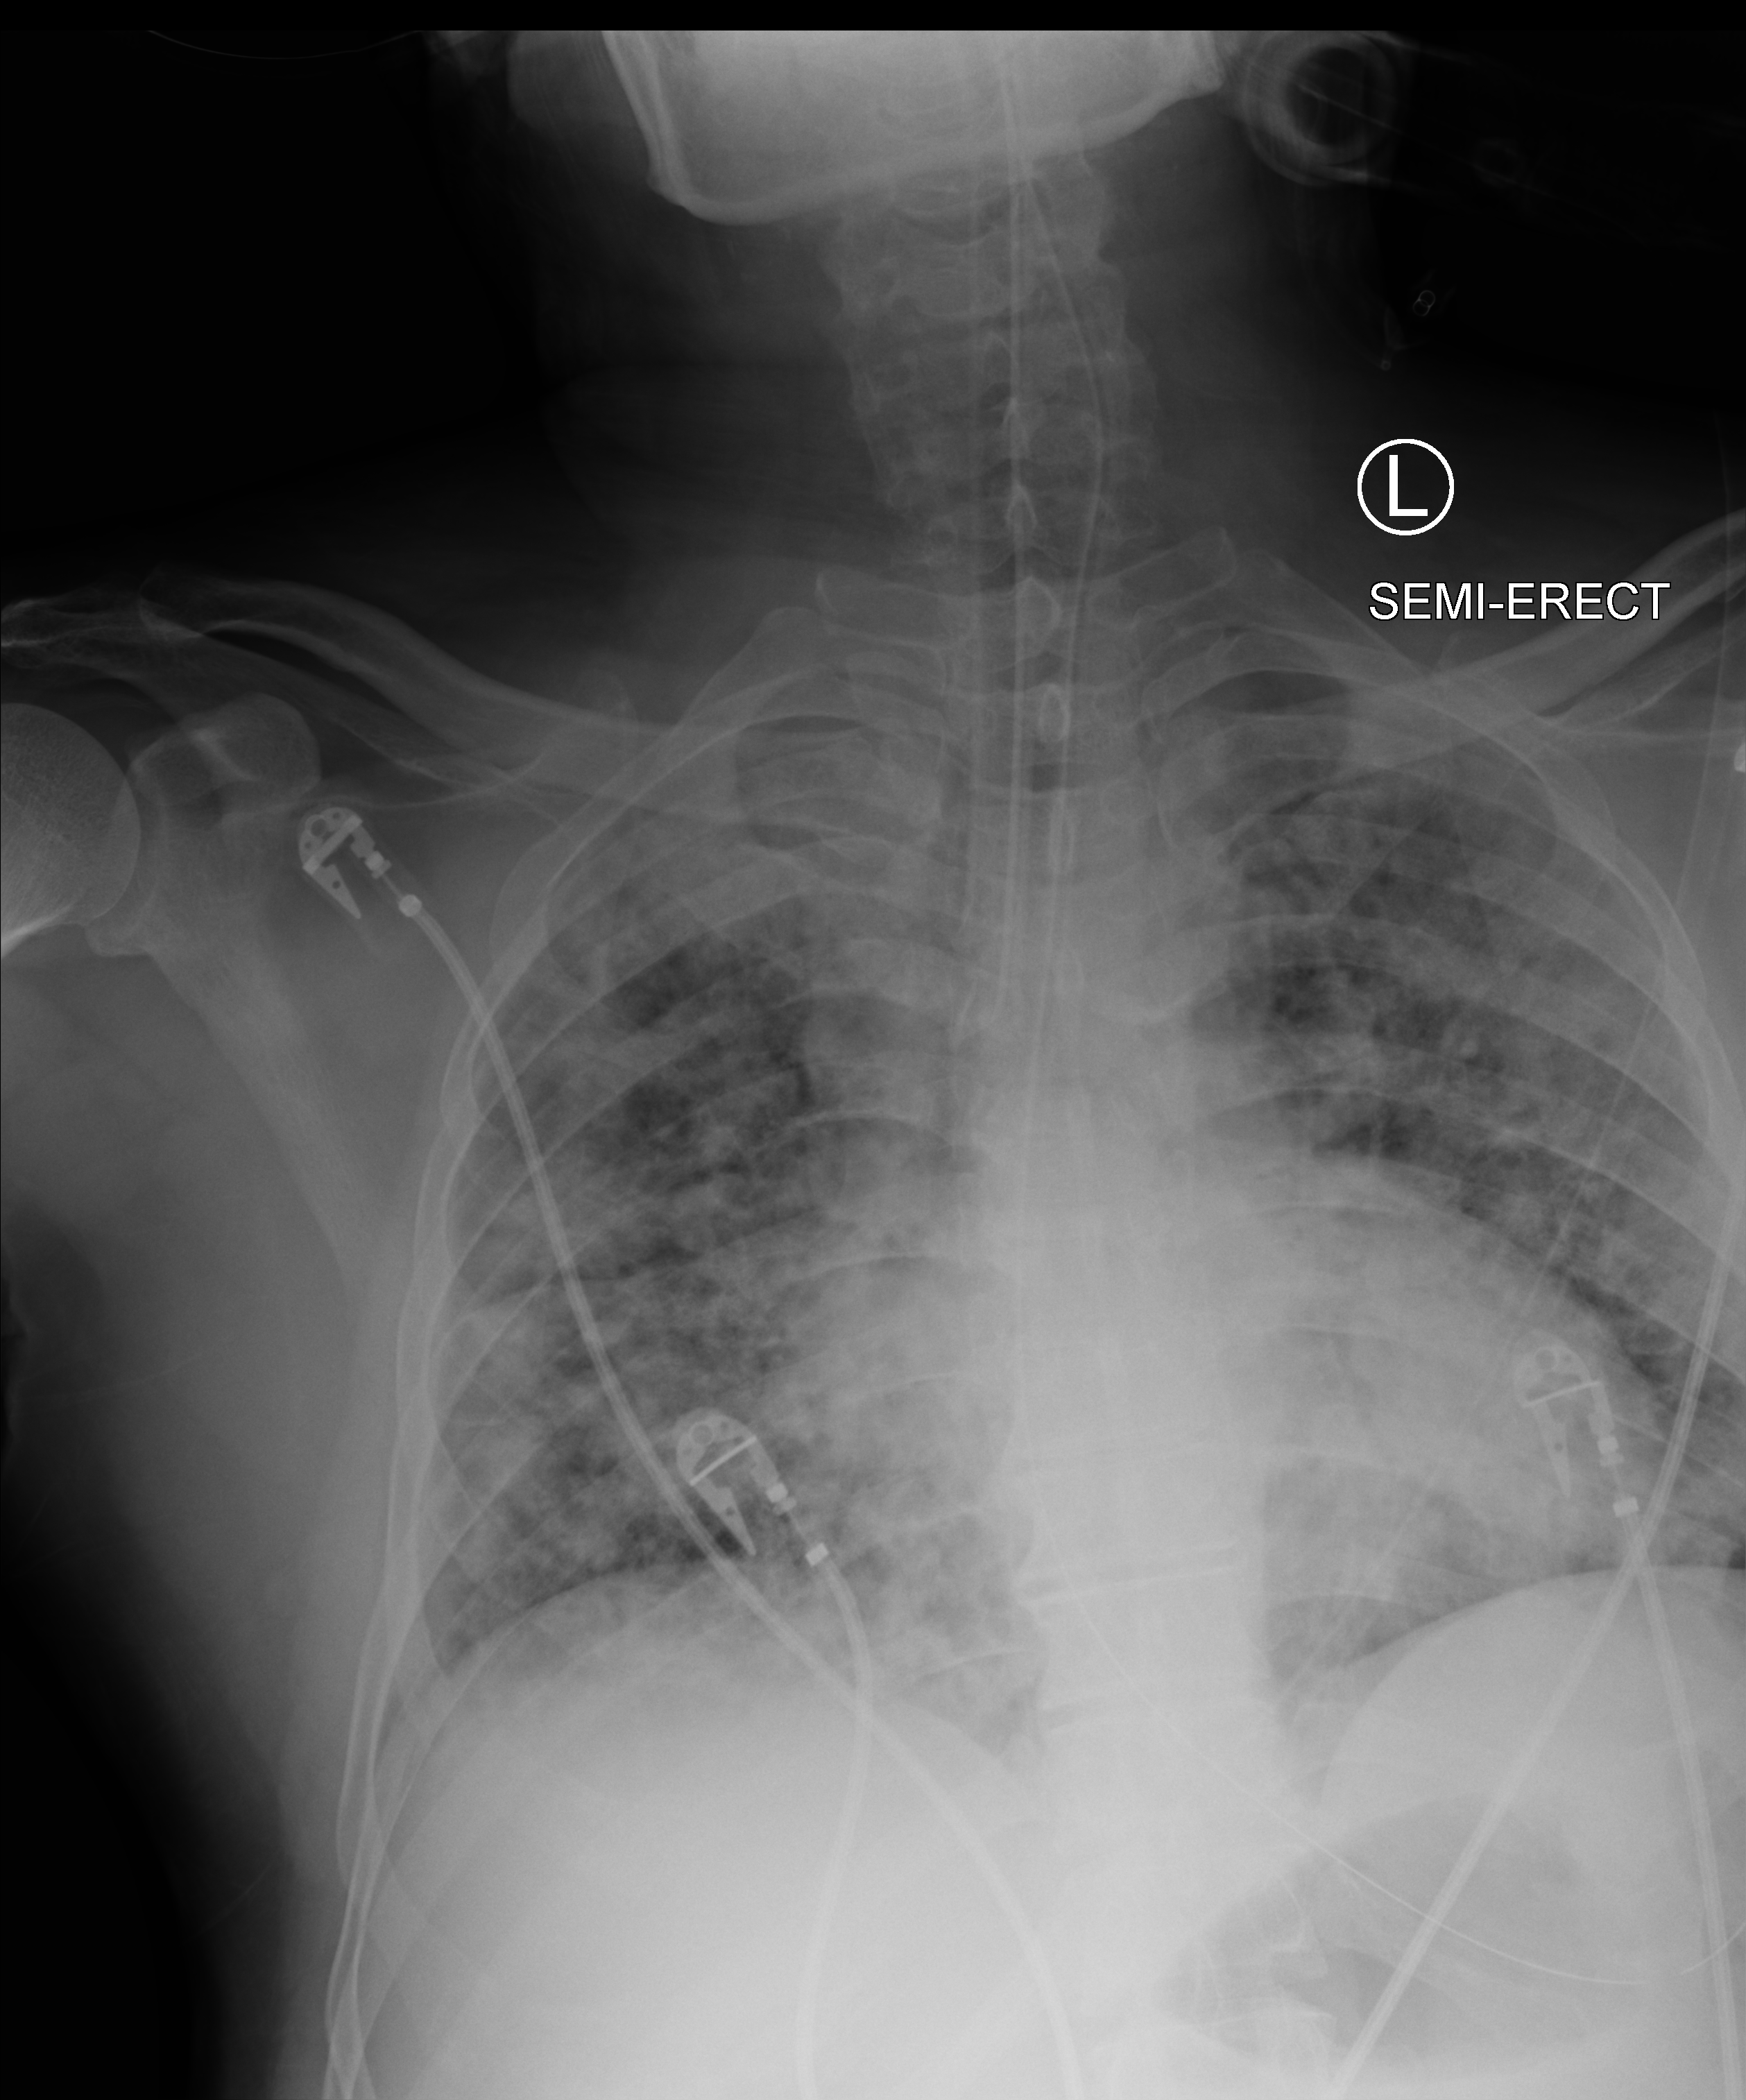
Portable chest radiograph, anteroposterior (AP) projection. Male patient hospitalised with COVID-19, age 18–59 years.
Hospital-stay facts (about this admission, not read from this image; timing relative to this image not recorded): length of hospital stay: 32 days; admitted to intensive care during this hospital stay: yes.